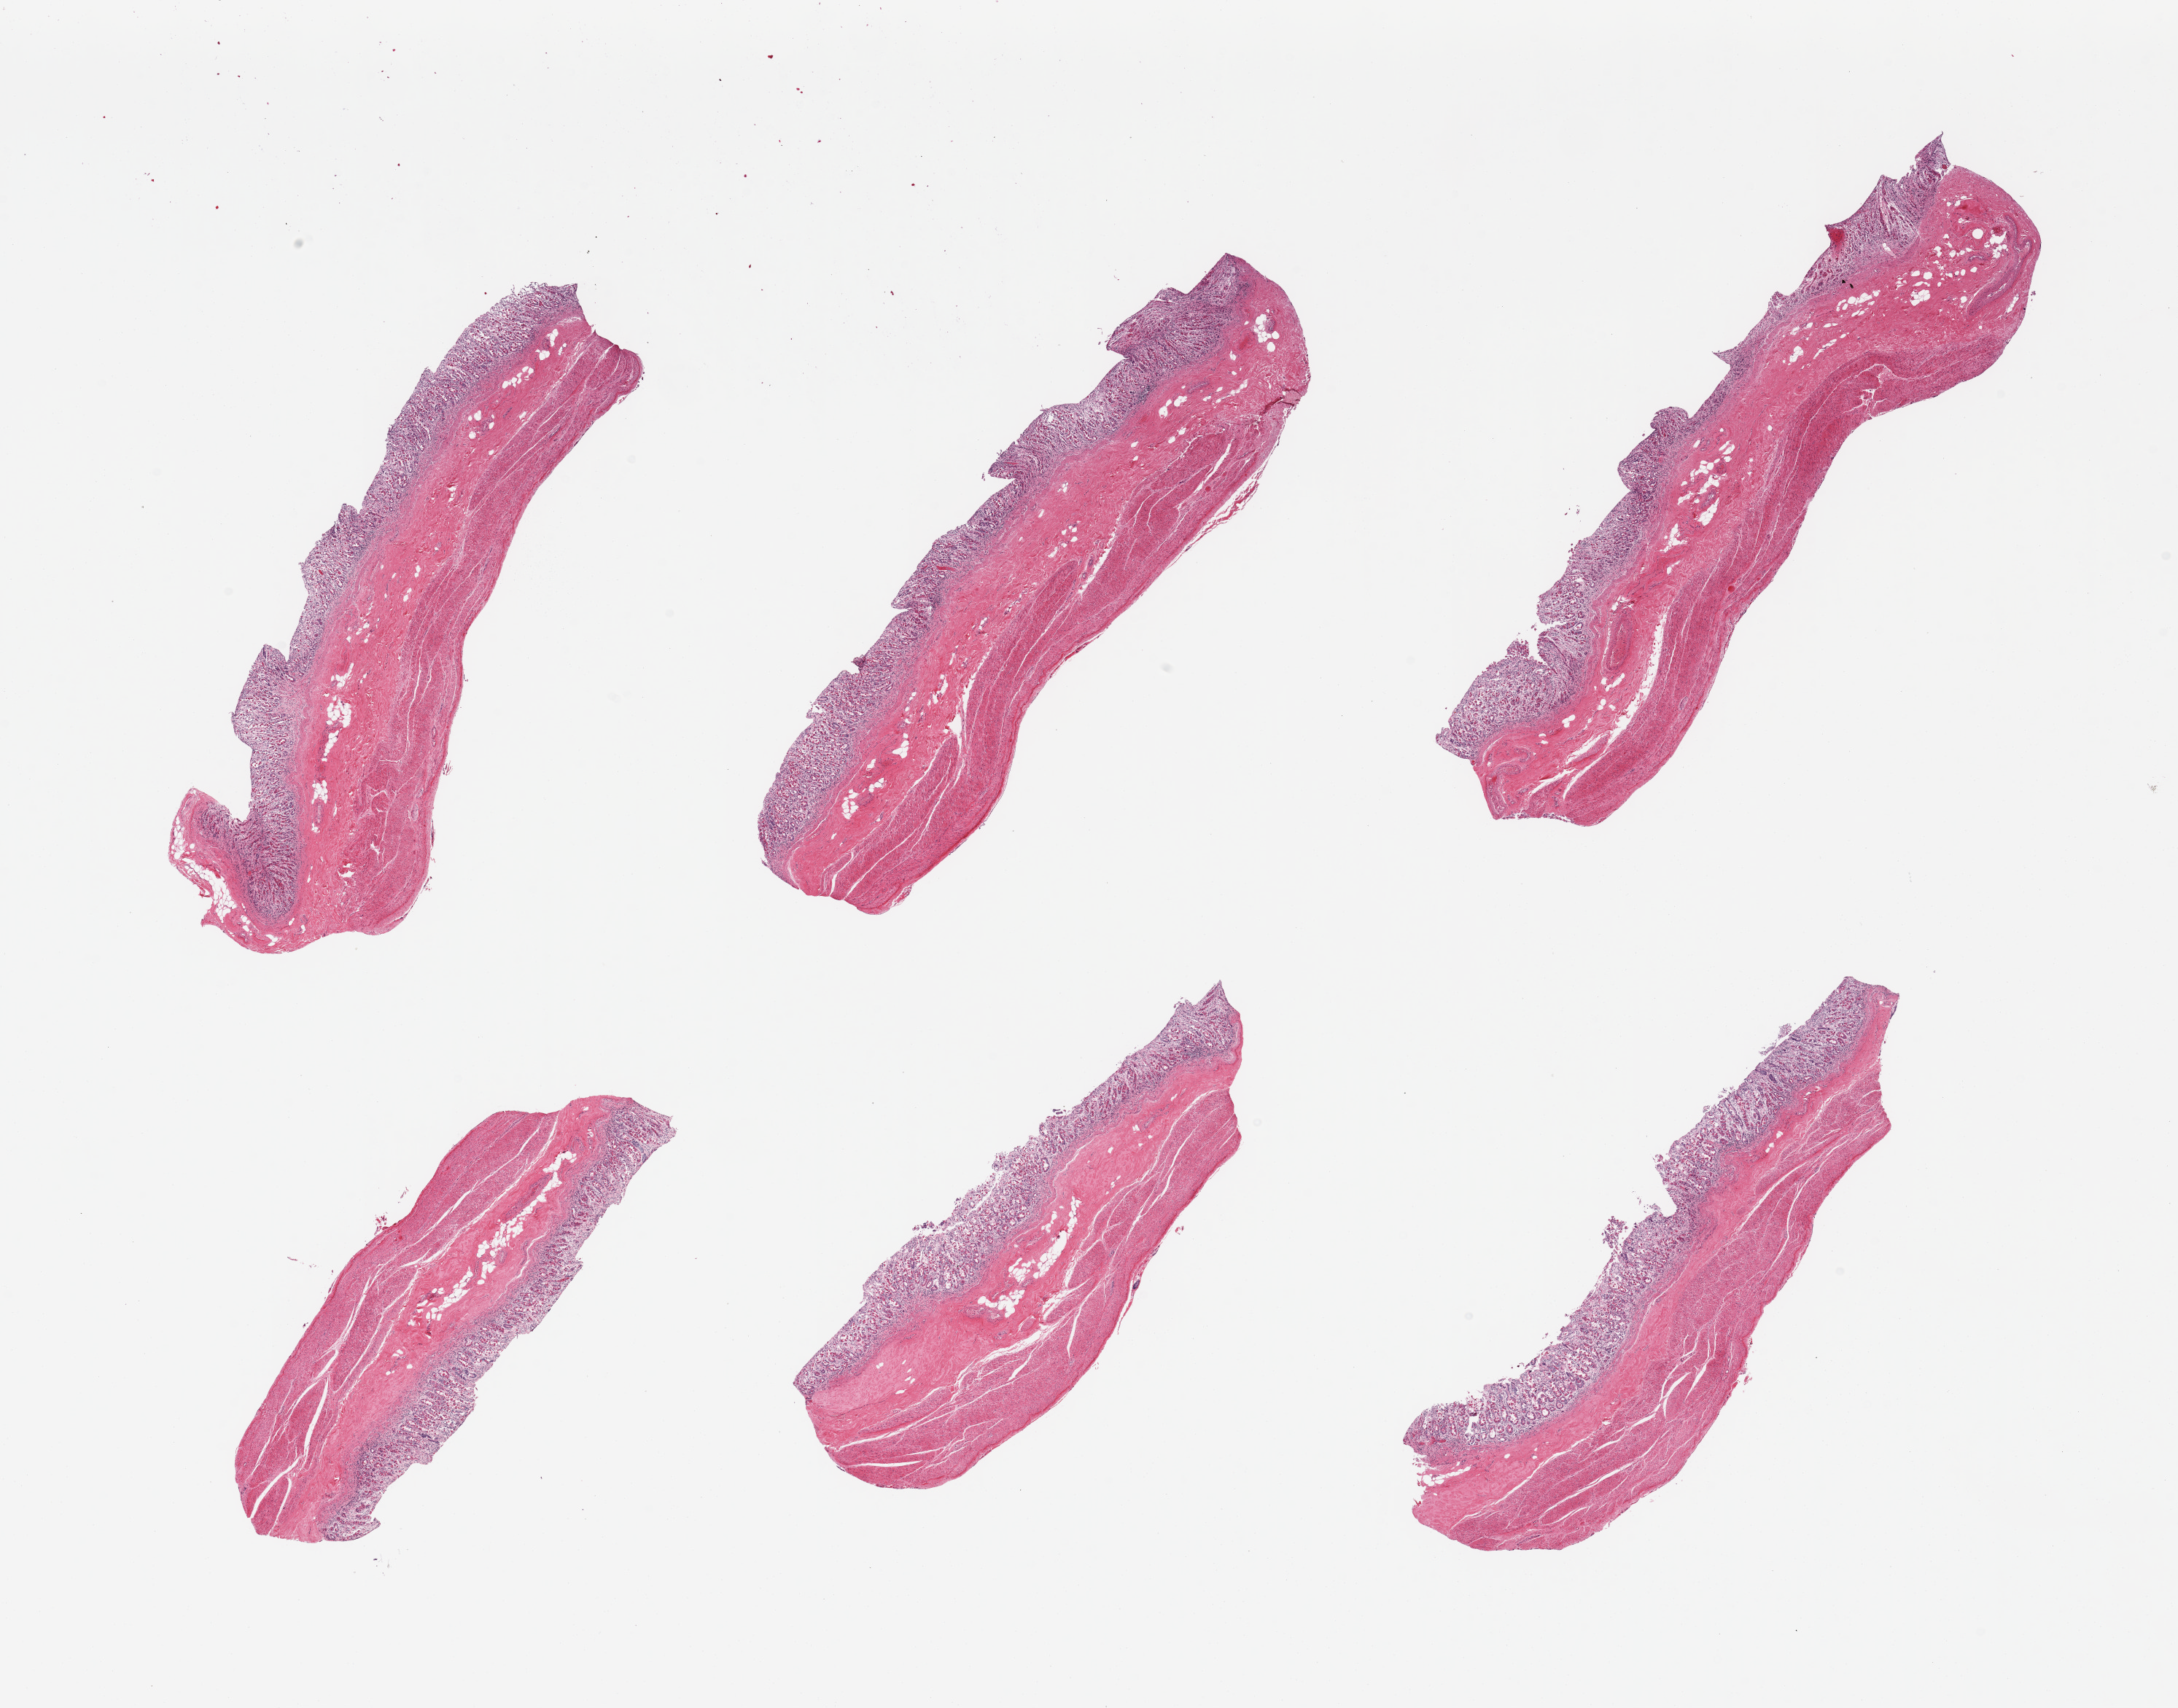
Whole-slide image, H&E stain, brightfield — low-resolution overview of the scanned area, about 23.6 x 18.5 mm, PAXgene-fixed, paraffin-embedded tissue, section of stomach (target tissue), donor tissue sample. Donor sex: female.
Pathologist's review note for this sample: 6 pieces, mucosa up to ~0.7mm, moderately-advanced autolysis.